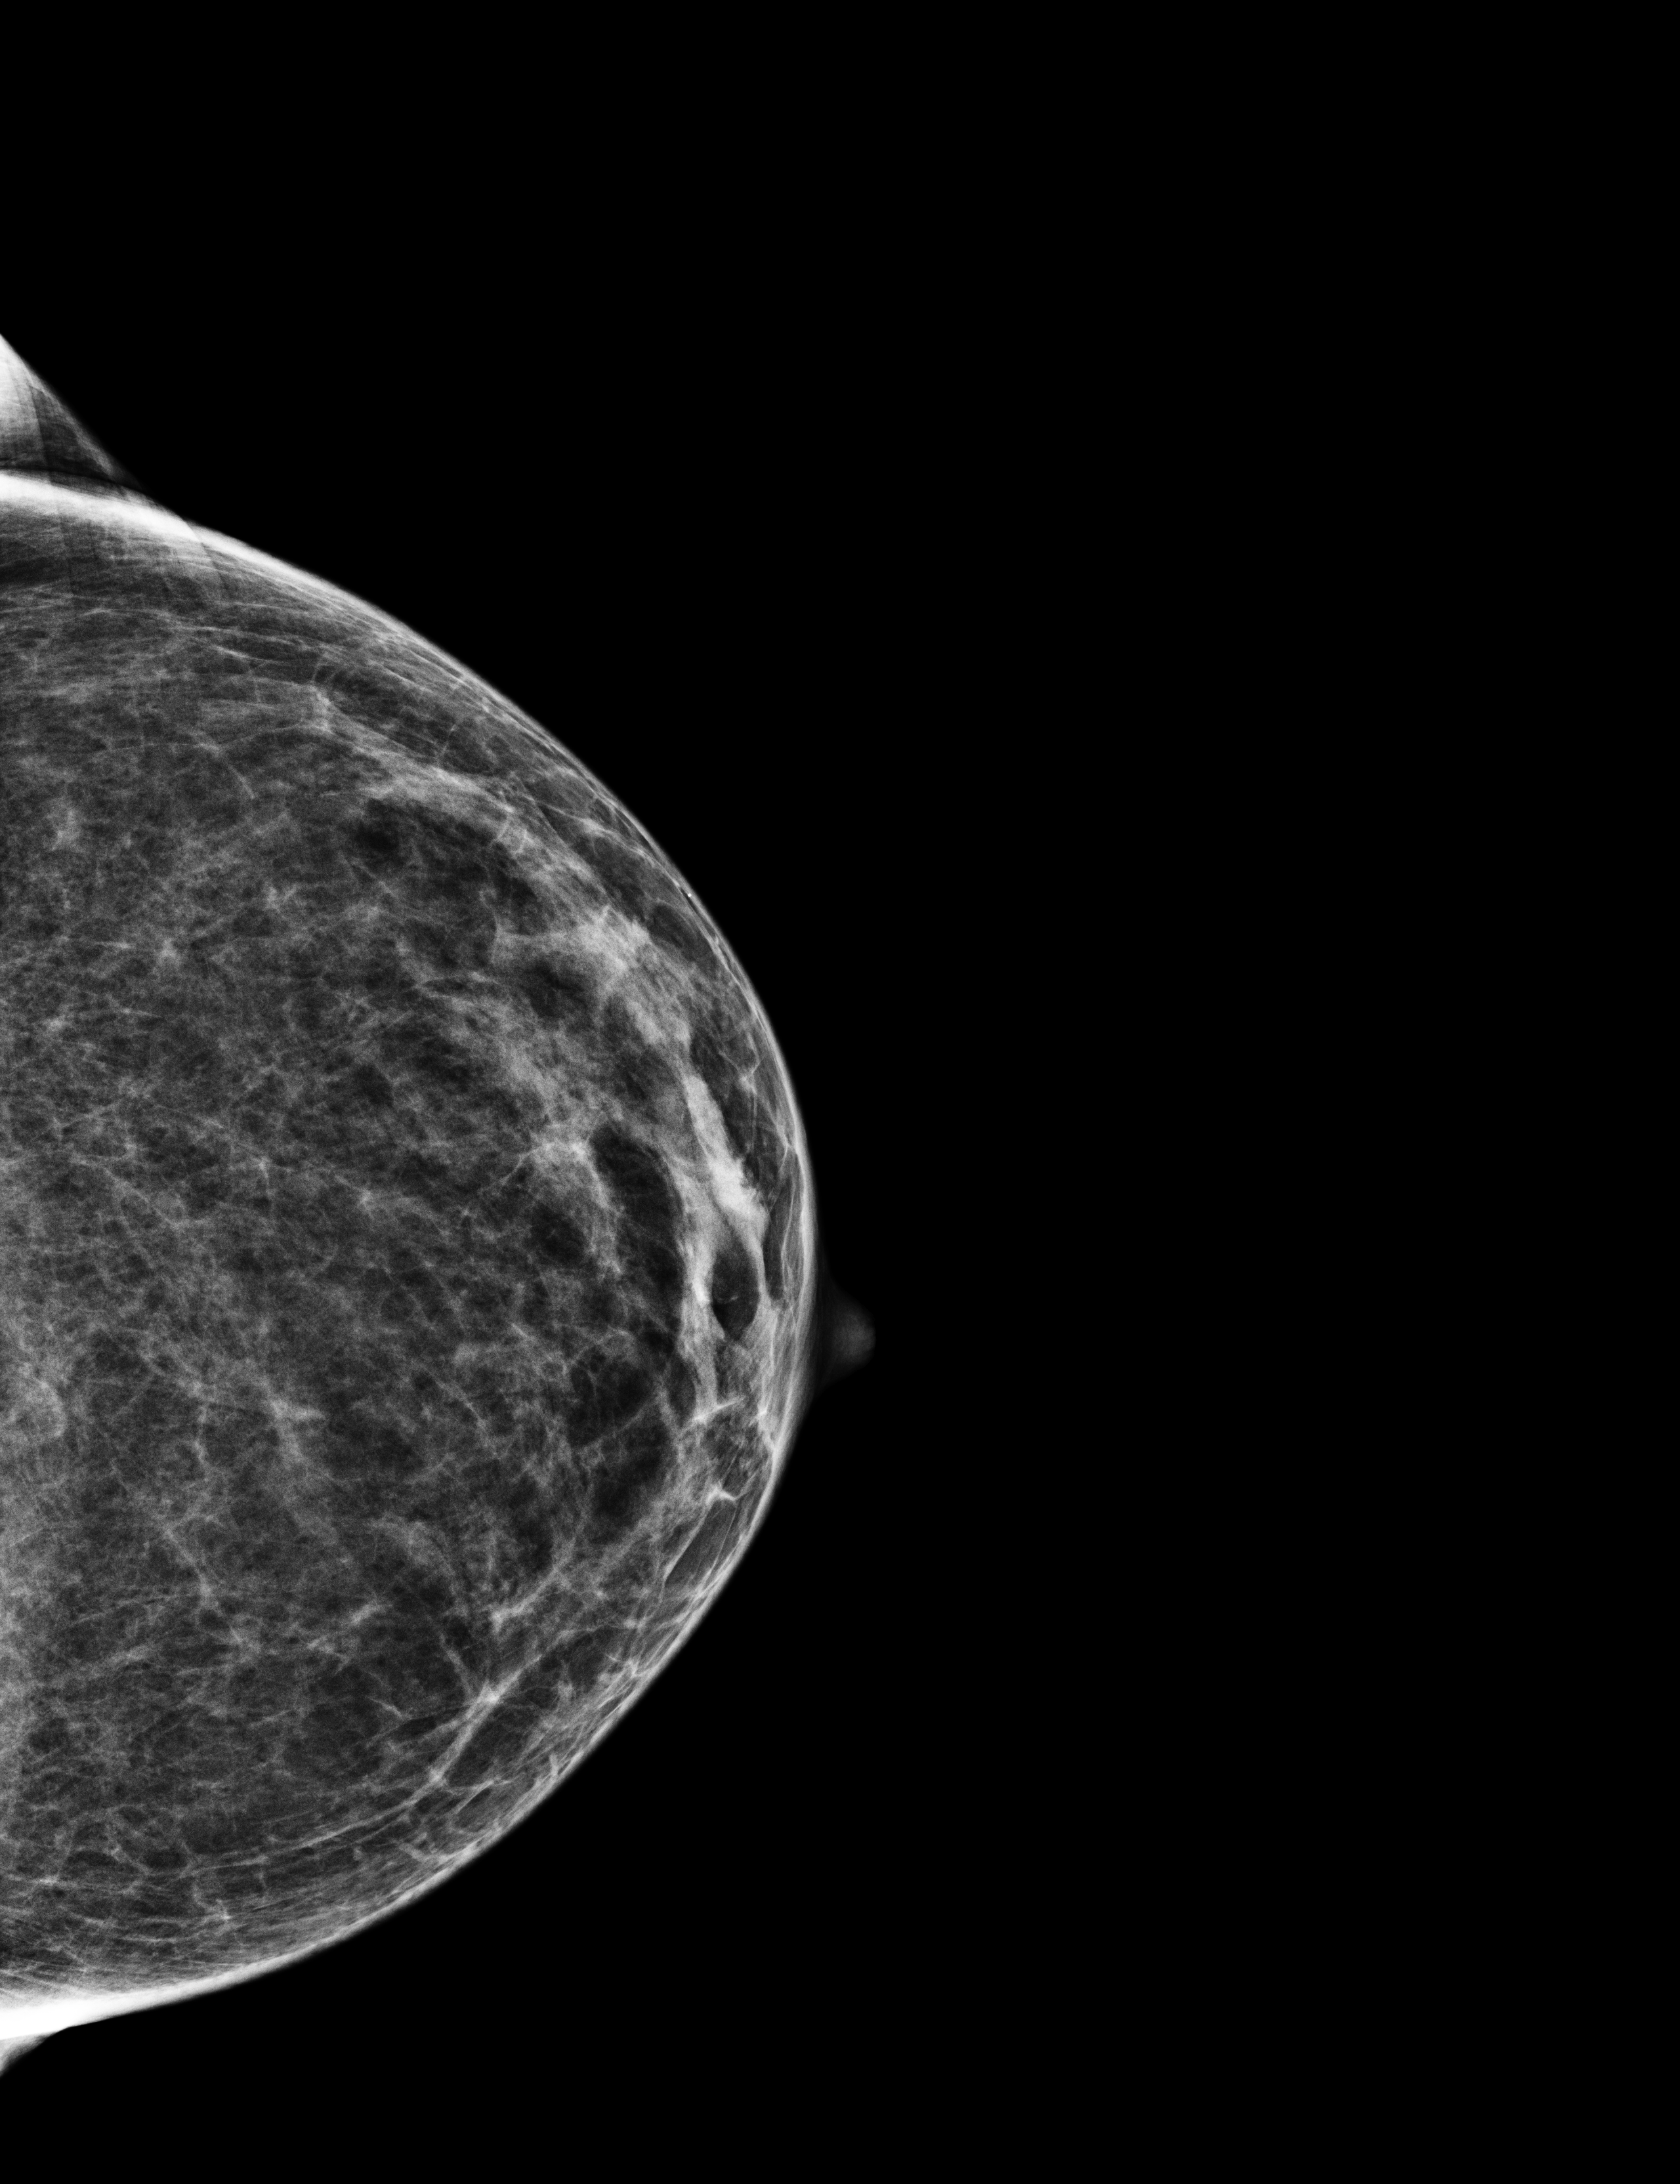
Annual screening mammography examination, compressed breast thickness 40 mm.
Image type: full-field digital mammogram. Breast: left. Projection: cranio-caudal projection.